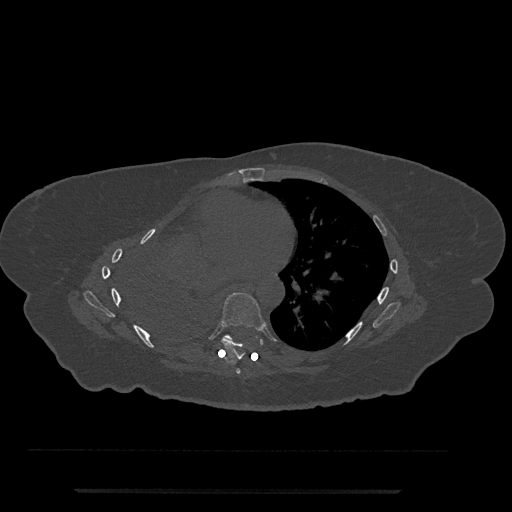
CT including the spine, one axial slice. Position 431 of 797 along the scan axis. Reconstruction kernel Br40s/3. 120 kVp. Bone window (W 1800 / L 400 HU). 0.5 mm slice thickness. 512 × 512 image matrix, field of view 440 × 440 mm. Female patient, age 51 years. From the clinical record (not read from this slice): primary cancer: neuro.
Structures marked on this image (semi-automatically segmented with operator editing):
- T6 vertebra: bounding box [x1, y1, x2, y2] px = [236, 369, 241, 374]
- T7 vertebra: [221, 292, 265, 360]
- T8 vertebra: [223, 335, 233, 339]